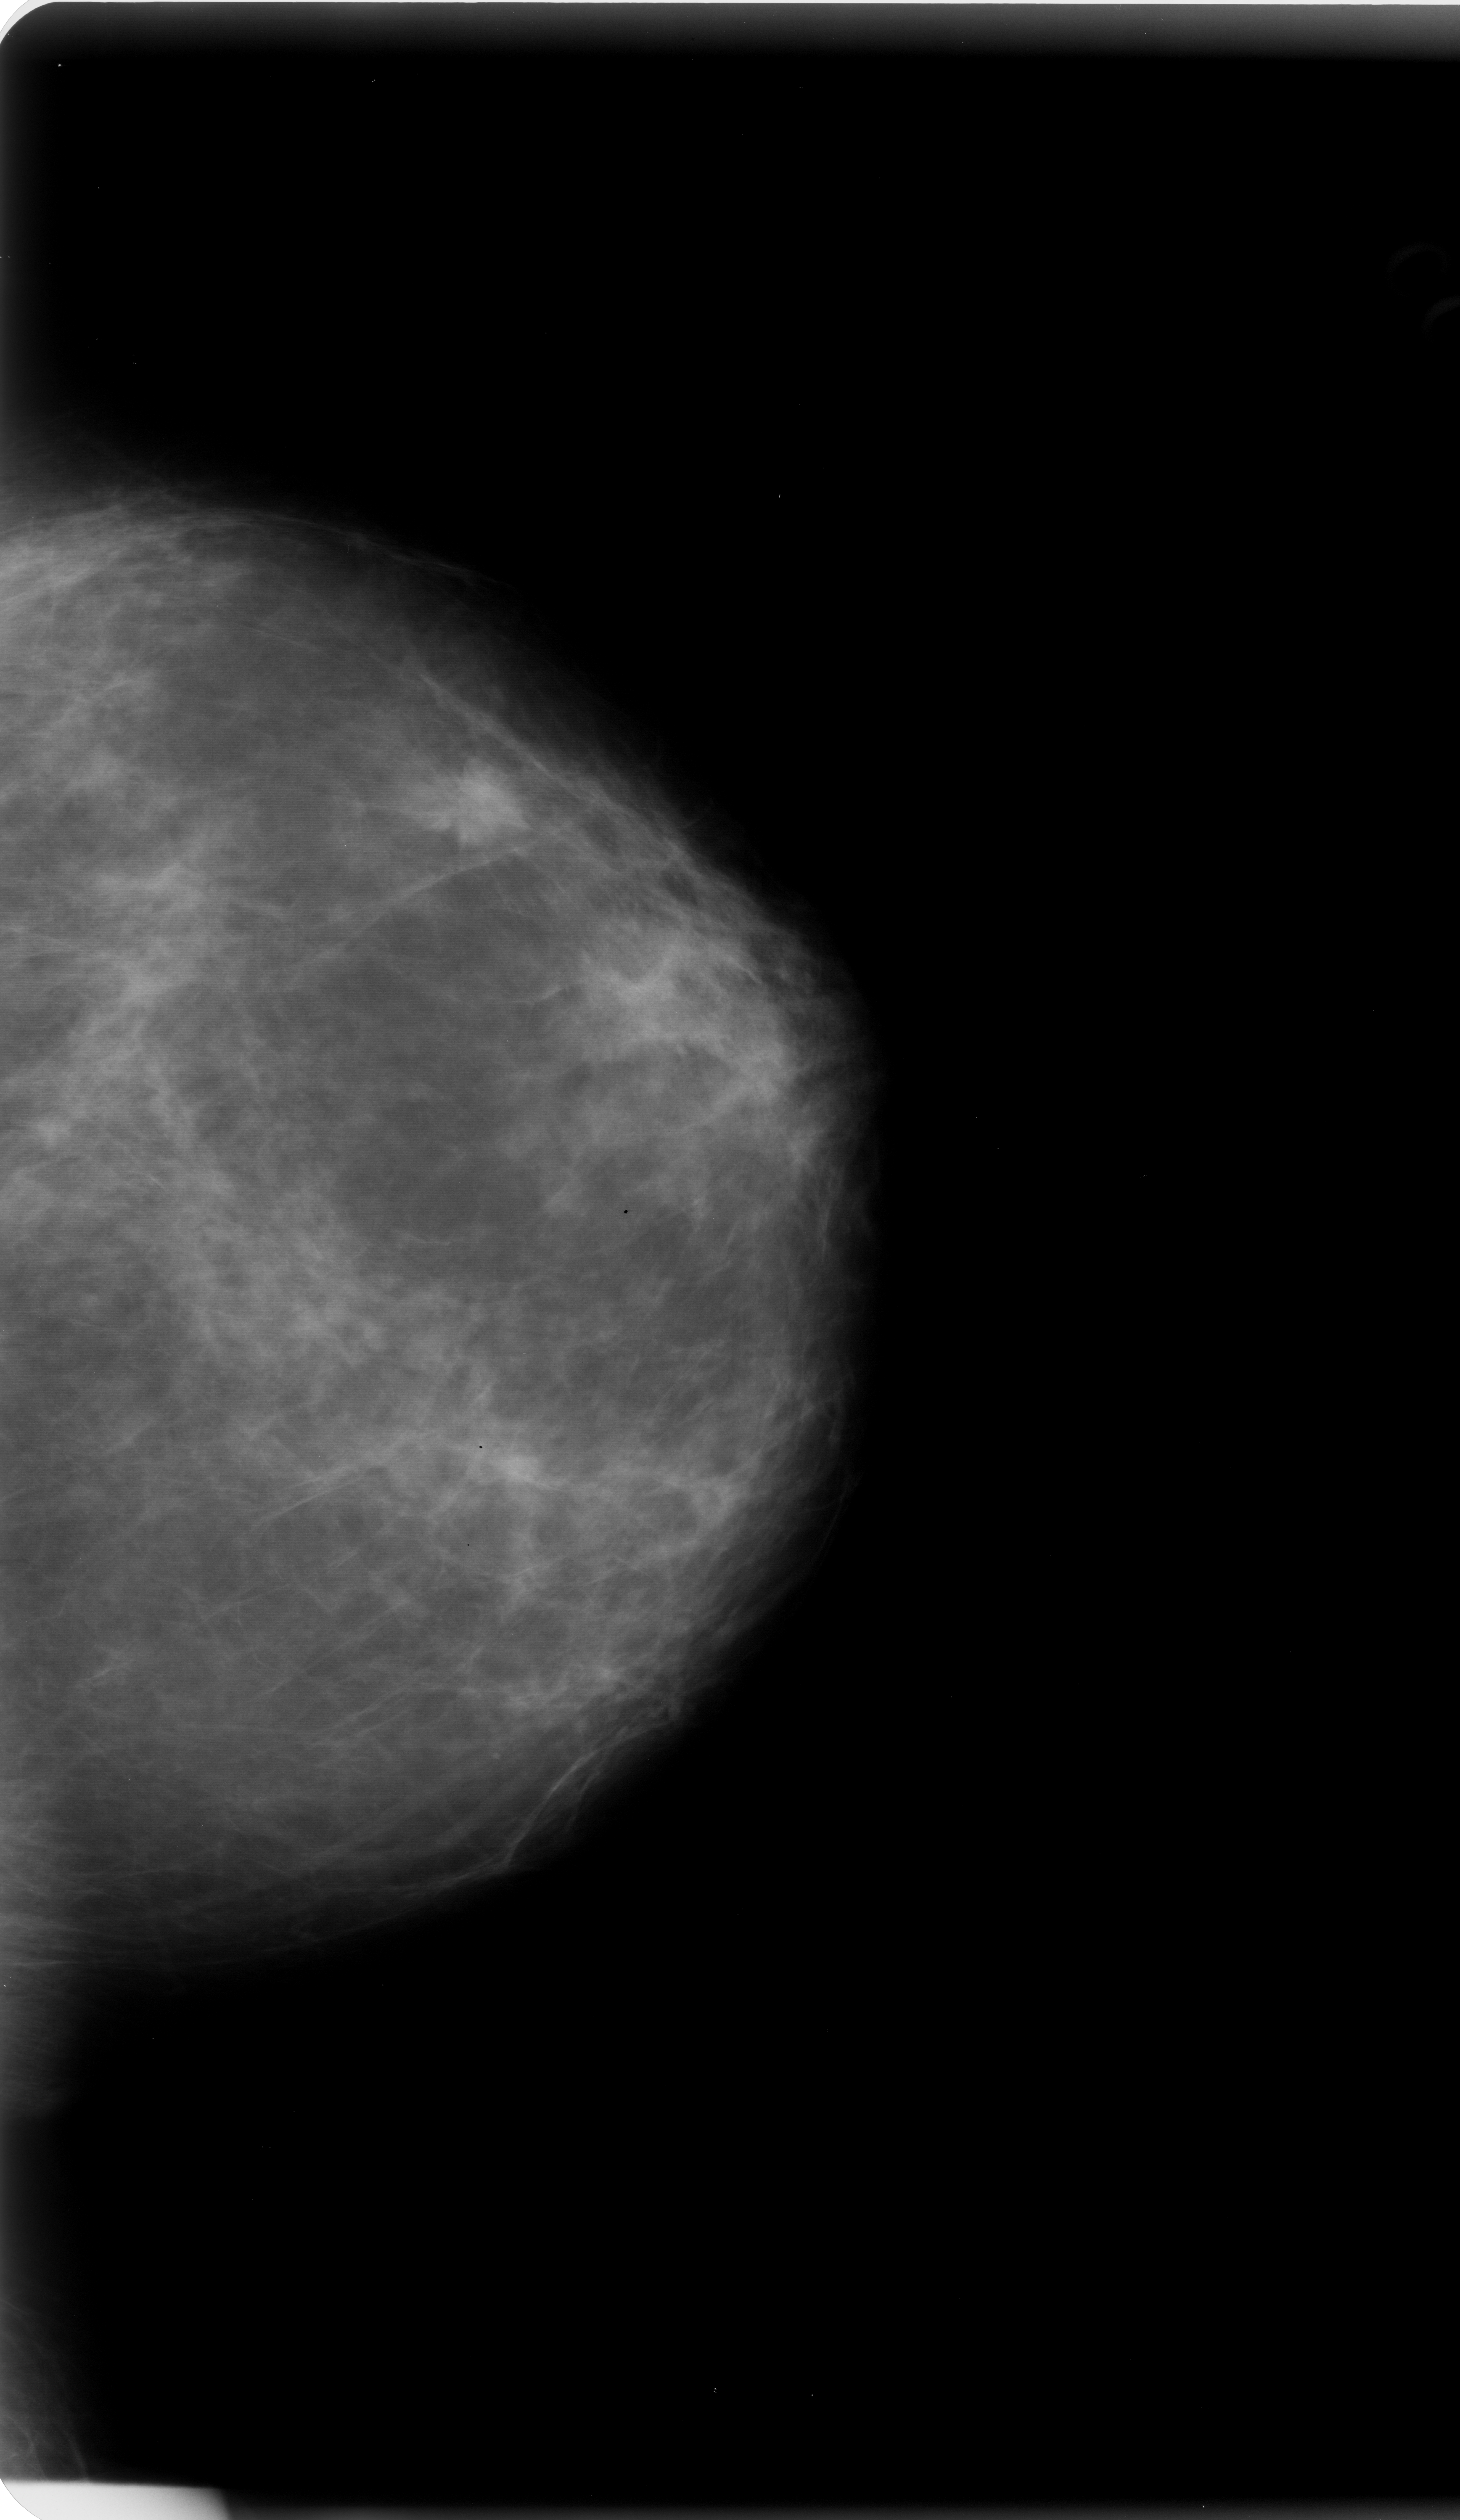
Digitized screen-film mammogram. Left breast. Craniocaudal (CC) view. Breast composition: scattered fibroglandular densities (BI-RADS density category 2 of 4). 1460 × 2520 image matrix.
Expert-marked regions of interest on this image (one box per marked abnormality):
- mass, shape round, margins spiculated; BI-RADS assessment category 5; subtlety rating 5 on a 1 (subtle) to 5 (obvious) scale; pathology result (as recorded, not read from the image): malignant: box from (x=431, y=759) to (x=522, y=855) px